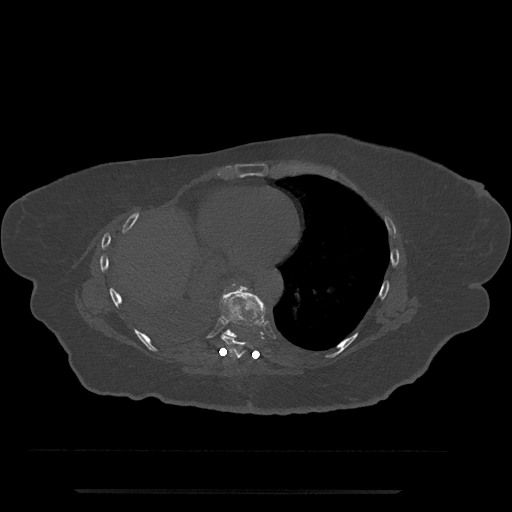
CT including the spine, one axial slice. Slice 377 of 797 in the series (ordered by position). Reconstruction kernel Br40s/3. 120 kVp. Bone window (W 1800 / L 400 HU). 0.5 mm slice thickness. 512 × 512 image matrix, field of view 440 × 440 mm. Female patient, age 51 years. Case-level facts recorded for this patient, not image findings: primary cancer: neuro.
Annotated regions visible in this slice (semi-automatically segmented with operator editing):
- T8 vertebra: bounding box (x1, y1, x2, y2) in pixels: (219, 284, 266, 359)
- T9 vertebra: (218, 284, 265, 340)